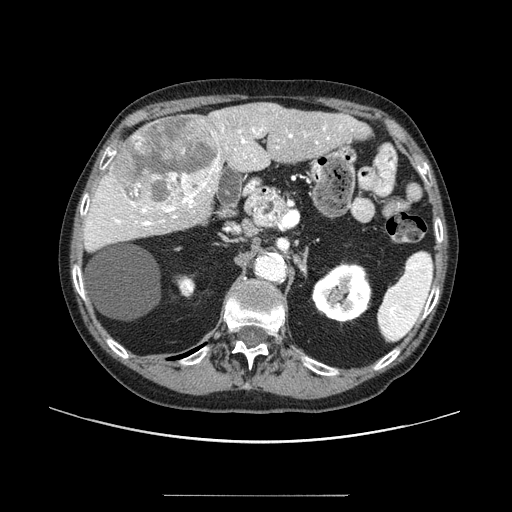
Contrast-enhanced abdominal CT (liver protocol), one axial slice; position 49 of 91 along the scan axis; 100 kVp; one of 2 acquisitions stored at this slice position; soft-tissue window (W 400 / L 40 HU); 2.5 mm slice thickness; 512 × 512 image matrix, field of view 400 × 400 mm. From the clinical record (not read from this slice): diagnosis: hepatocellular carcinoma (patient treated with transarterial chemoembolisation; whether this scan precedes or follows treatment is not stated here); TNM stage (as recorded): Stage-I; Child-Pugh class: A; tumour differentiation: moderately differentiated.
Outlined on this slice (semi-automatically segmented with operator editing):
- liver parenchyma outside the tumour (the mass and vessels are separate outlines, so this box may not span the whole liver): bounding box <84,102,370,250> (left, top, right, bottom; pixels)
- mass: <112,114,220,210>
- liver vessels: <89,127,329,226>